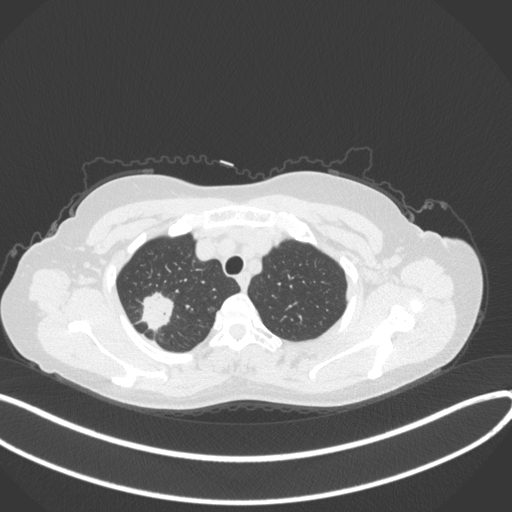
Chest CT, one axial slice. Reconstruction kernel B31f. Lung window (W 1500 / L -600 HU). 1 mm slice thickness. 512 × 512 image matrix, field of view 400 × 400 mm. Female patient, age 50 years. From the clinical record (not read from this slice): clinical TNM (as recorded): T1c N0 M0.
Annotated regions visible in this slice (rectangle marked by the reading radiologist):
- lung tumour (recorded histology: adenocarcinoma): bounding box [x1, y1, x2, y2] px = [137, 289, 176, 332]